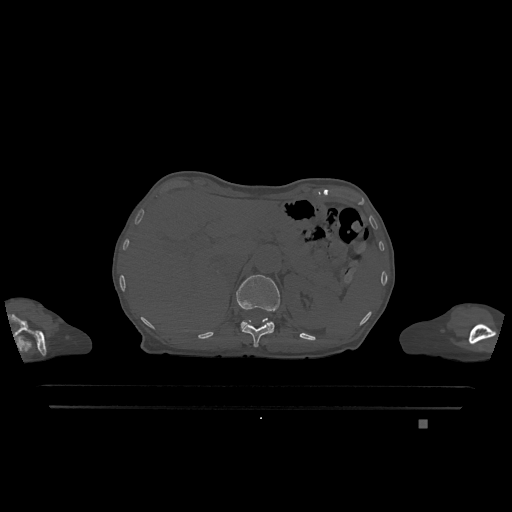
CT including the spine, one axial slice. Position 506 of 1317 along the scan axis. Bone window (W 1800 / L 400 HU). 0.5 mm slice thickness. 512 × 512 image matrix, field of view 500 × 500 mm. Patient: female, 74 years. Case-level facts recorded for this patient, not image findings: primary cancer: lung.
Annotated regions visible in this slice (semi-automatic segmentation, software-assisted and operator-edited):
- L1 vertebra: bounding box (x1, y1, x2, y2) in pixels: (236, 275, 280, 333)
- T12 vertebra: (242, 318, 272, 347)